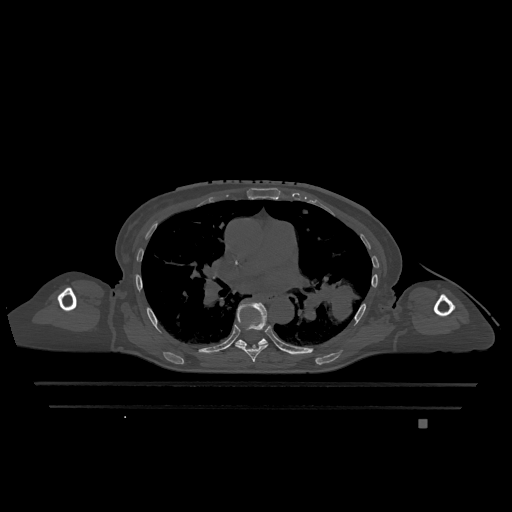
CT including the spine, one axial slice. Slice 769 of 1317 in the series (ordered by position). Bone window (W 1800 / L 400 HU). 0.5 mm slice thickness. 512 × 512 image matrix. Patient: female, 74 years. From the clinical record (not read from this slice): primary cancer: lung; vertebrae with lytic lesions (as recorded): T1, T4, T5, T6, L4, L5.
Structures marked on this image (semi-automatically segmented with operator editing):
- T6 vertebra: bounding box (x1, y1, x2, y2) in pixels: (236, 302, 269, 362)
- T7 vertebra: (235, 338, 268, 346)